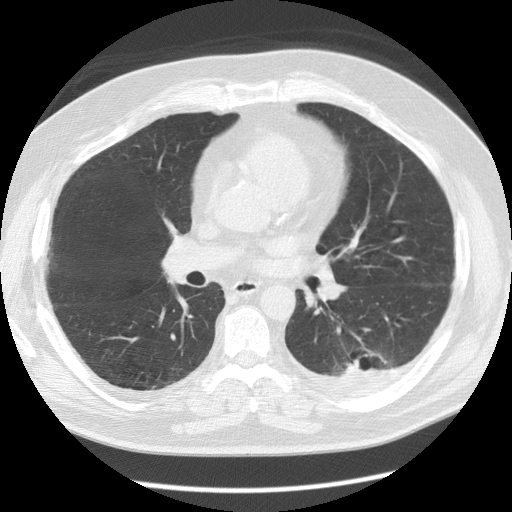
Chest CT (low-dose screening protocol), one axial image. First (baseline) screen. Lung window (W 1500 / L -600 HU). Standard (soft-tissue) reconstruction kernel (STANDARD). 512 × 512 image matrix, field of view 370 × 370 mm. Male participant, aged 56 years at enrolment. Former smoker at enrolment.
Expert-annotated lung lesion, box from (x=324, y=341) to (x=396, y=394) px. The screening reader recorded 4 non-calcified nodules or masses ≥4 mm on this exam (left lower lobe, left lower lobe, right middle lobe, left upper lobe); which of them this box marks is not recorded. Lung cancer was diagnosed 173 days after this screen: non-small cell carcinoma, left lower lobe, stage IV (AJCC 6th edition), 50 mm at pathology.